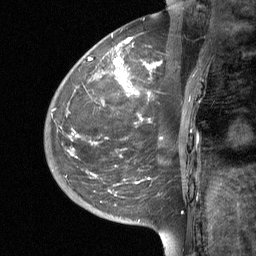
Breast MRI (dynamic contrast-enhanced), one sagittal slice; slice 13 of 64 in the series (ordered by position); dynamic contrast-enhanced study with each time point stored as its own series, time point 2 of 3 at this slice position (early post-contrast, ordered by acquisition time); 1.5 T; TE 4.8 ms, TR 27 ms; 256 × 256 image matrix. Female patient, age 42 years. Case-level facts recorded for this patient, not image findings: setting: breast cancer imaged before/during neoadjuvant chemotherapy; receptor status: triple-negative.
Outlined on this slice (semi-automatic segmentation, software-assisted and operator-edited):
- analysis volume of interest (the breast-tissue region the enhancement analysis was run in; not a lesion): bounding box <44,29,203,190> (left, top, right, bottom; pixels)
- tumour enhancement mask (voxels above the 90 % enhancement threshold inside the analysis volume of interest): <87,37,162,184>